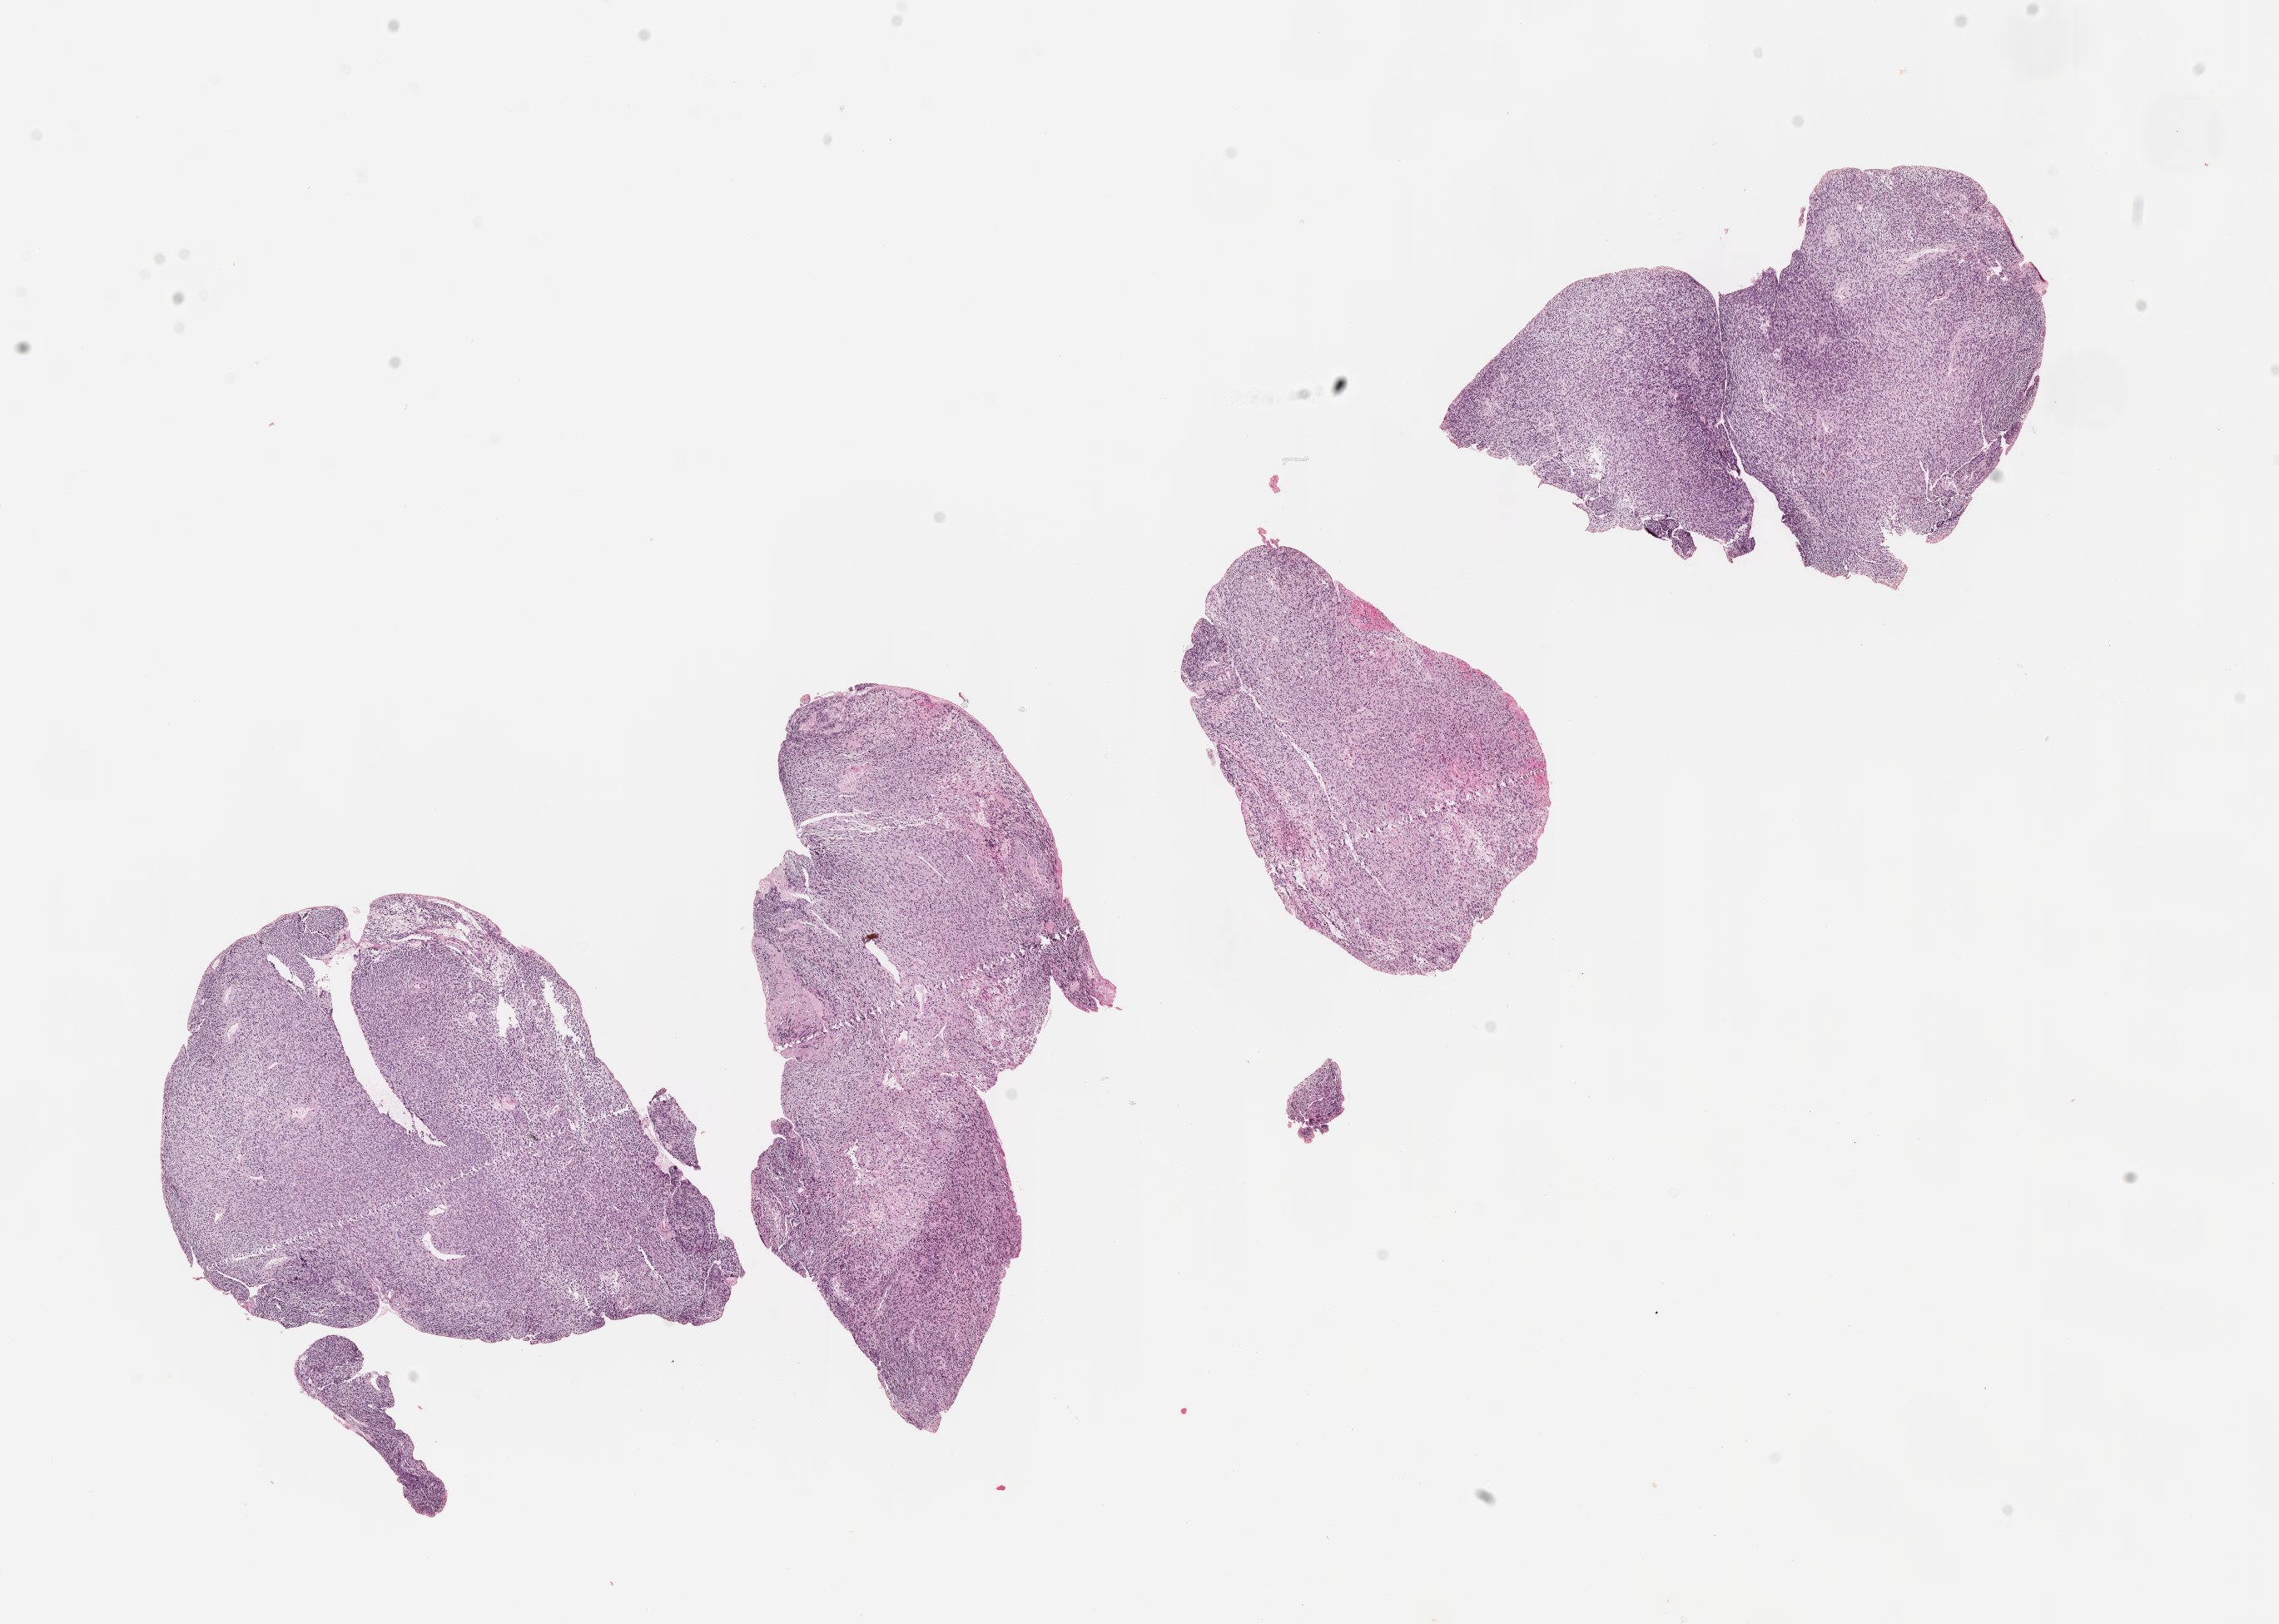
Digitized hematoxylin and eosin (H&E)-stained section of tumor tissue — low-resolution overview of the scanned area, about 11.1 x 7.9 mm, formalin-fixed, paraffin-embedded (FFPE) tissue, sample anatomic site: bladder. Patient: male, age 0.6 years at diagnosis.
* stage (as recorded): 3
* diagnosis: rhabdomyosarcoma; histological classification: embryonal rhabdomyosarcoma